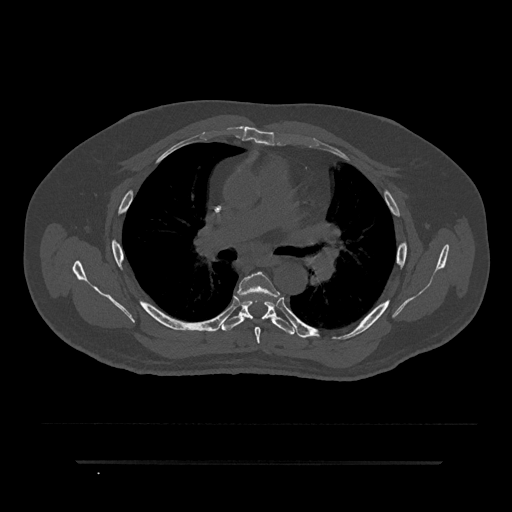
CT including the spine, one axial slice; position 550 of 797 along the scan axis; reconstruction kernel Br40s/3; bone window (W 1800 / L 400 HU); 0.5 mm slice thickness; 512 × 512 image matrix. Patient: male, 59 years. From the clinical record (not read from this slice): primary cancer: bile ducts.
Outlined on this slice (semi-automatic segmentation, software-assisted and operator-edited):
- T5 vertebra: bounding box [x1, y1, x2, y2] px = [238, 271, 278, 344]
- T6 vertebra: [221, 300, 294, 335]